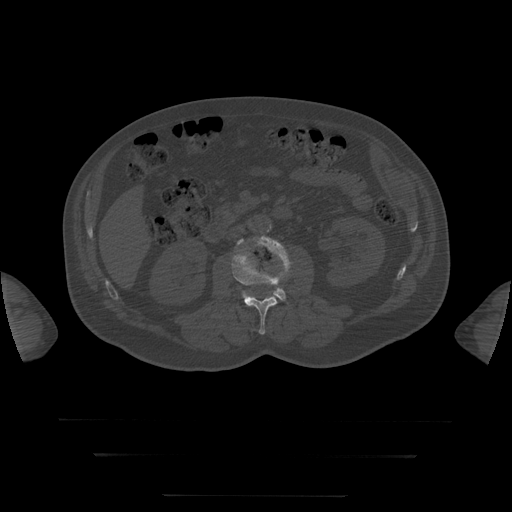
CT including the spine, one axial slice; position 15 of 397 along the scan axis; reconstruction kernel STANDARD; 120 kVp; bone window (W 1800 / L 400 HU); 512 × 512 image matrix. Patient age 73 years. Case-level facts recorded for this patient, not image findings: primary cancer: prostate.
Outlined on this slice (semi-automatically segmented with operator editing):
- L3 vertebra: bounding box <237,236,291,301> (left, top, right, bottom; pixels)